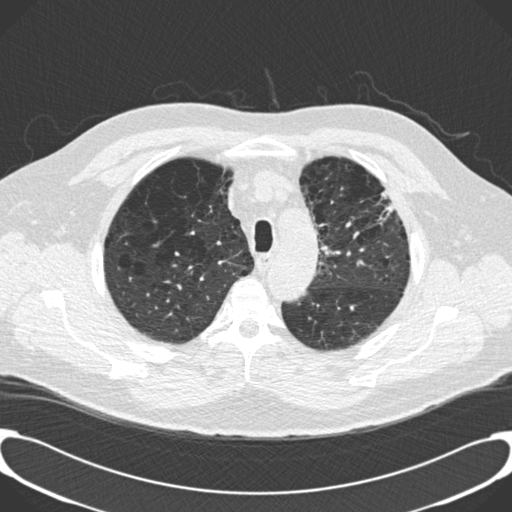
Axial slice from a low-dose chest CT screening exam, third annual screen, lung window (W 1500 / L -600 HU), 2 mm slice thickness, slice 33 of 189 in the series. Male, age 59 years at enrolment.
- Expert-annotated lung lesion, bounding box [x1, y1, x2, y2] px = [364, 178, 409, 230].
- Screening reader's record for this exam: no non-calcified nodule ≥4 mm recorded.
- Official screen result: positive, other.
- Lung cancer was diagnosed 134 days after this screen: bronchiolo-alveolar carcinoma, mixed mucinous and non-mucinous, left upper lobe, stage IA (AJCC 6th edition), 20 mm at pathology.